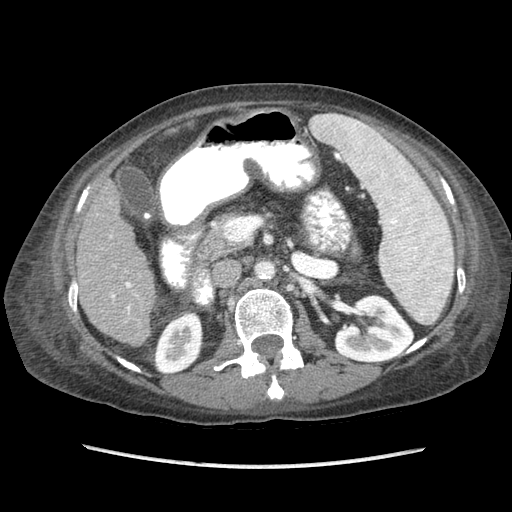
Contrast-enhanced abdominal CT (liver protocol), one axial slice. Reconstruction kernel STANDARD. 120 kVp. Soft-tissue window (W 400 / L 40 HU). 2.5 mm slice thickness. 512 × 512 image matrix, field of view 340 × 340 mm. Case-level facts recorded for this patient, not image findings: diagnosis: hepatocellular carcinoma (patient treated with transarterial chemoembolisation; whether this scan precedes or follows treatment is not stated here); TNM stage (as recorded): Stage-IIIB.
Structures marked on this image (semi-automatic segmentation, software-assisted and operator-edited):
- liver parenchyma outside the tumour (the mass and vessels are separate outlines, so this box may not span the whole liver): bounding box <76,181,156,346> (left, top, right, bottom; pixels)
- liver vessels: <110,236,136,314>